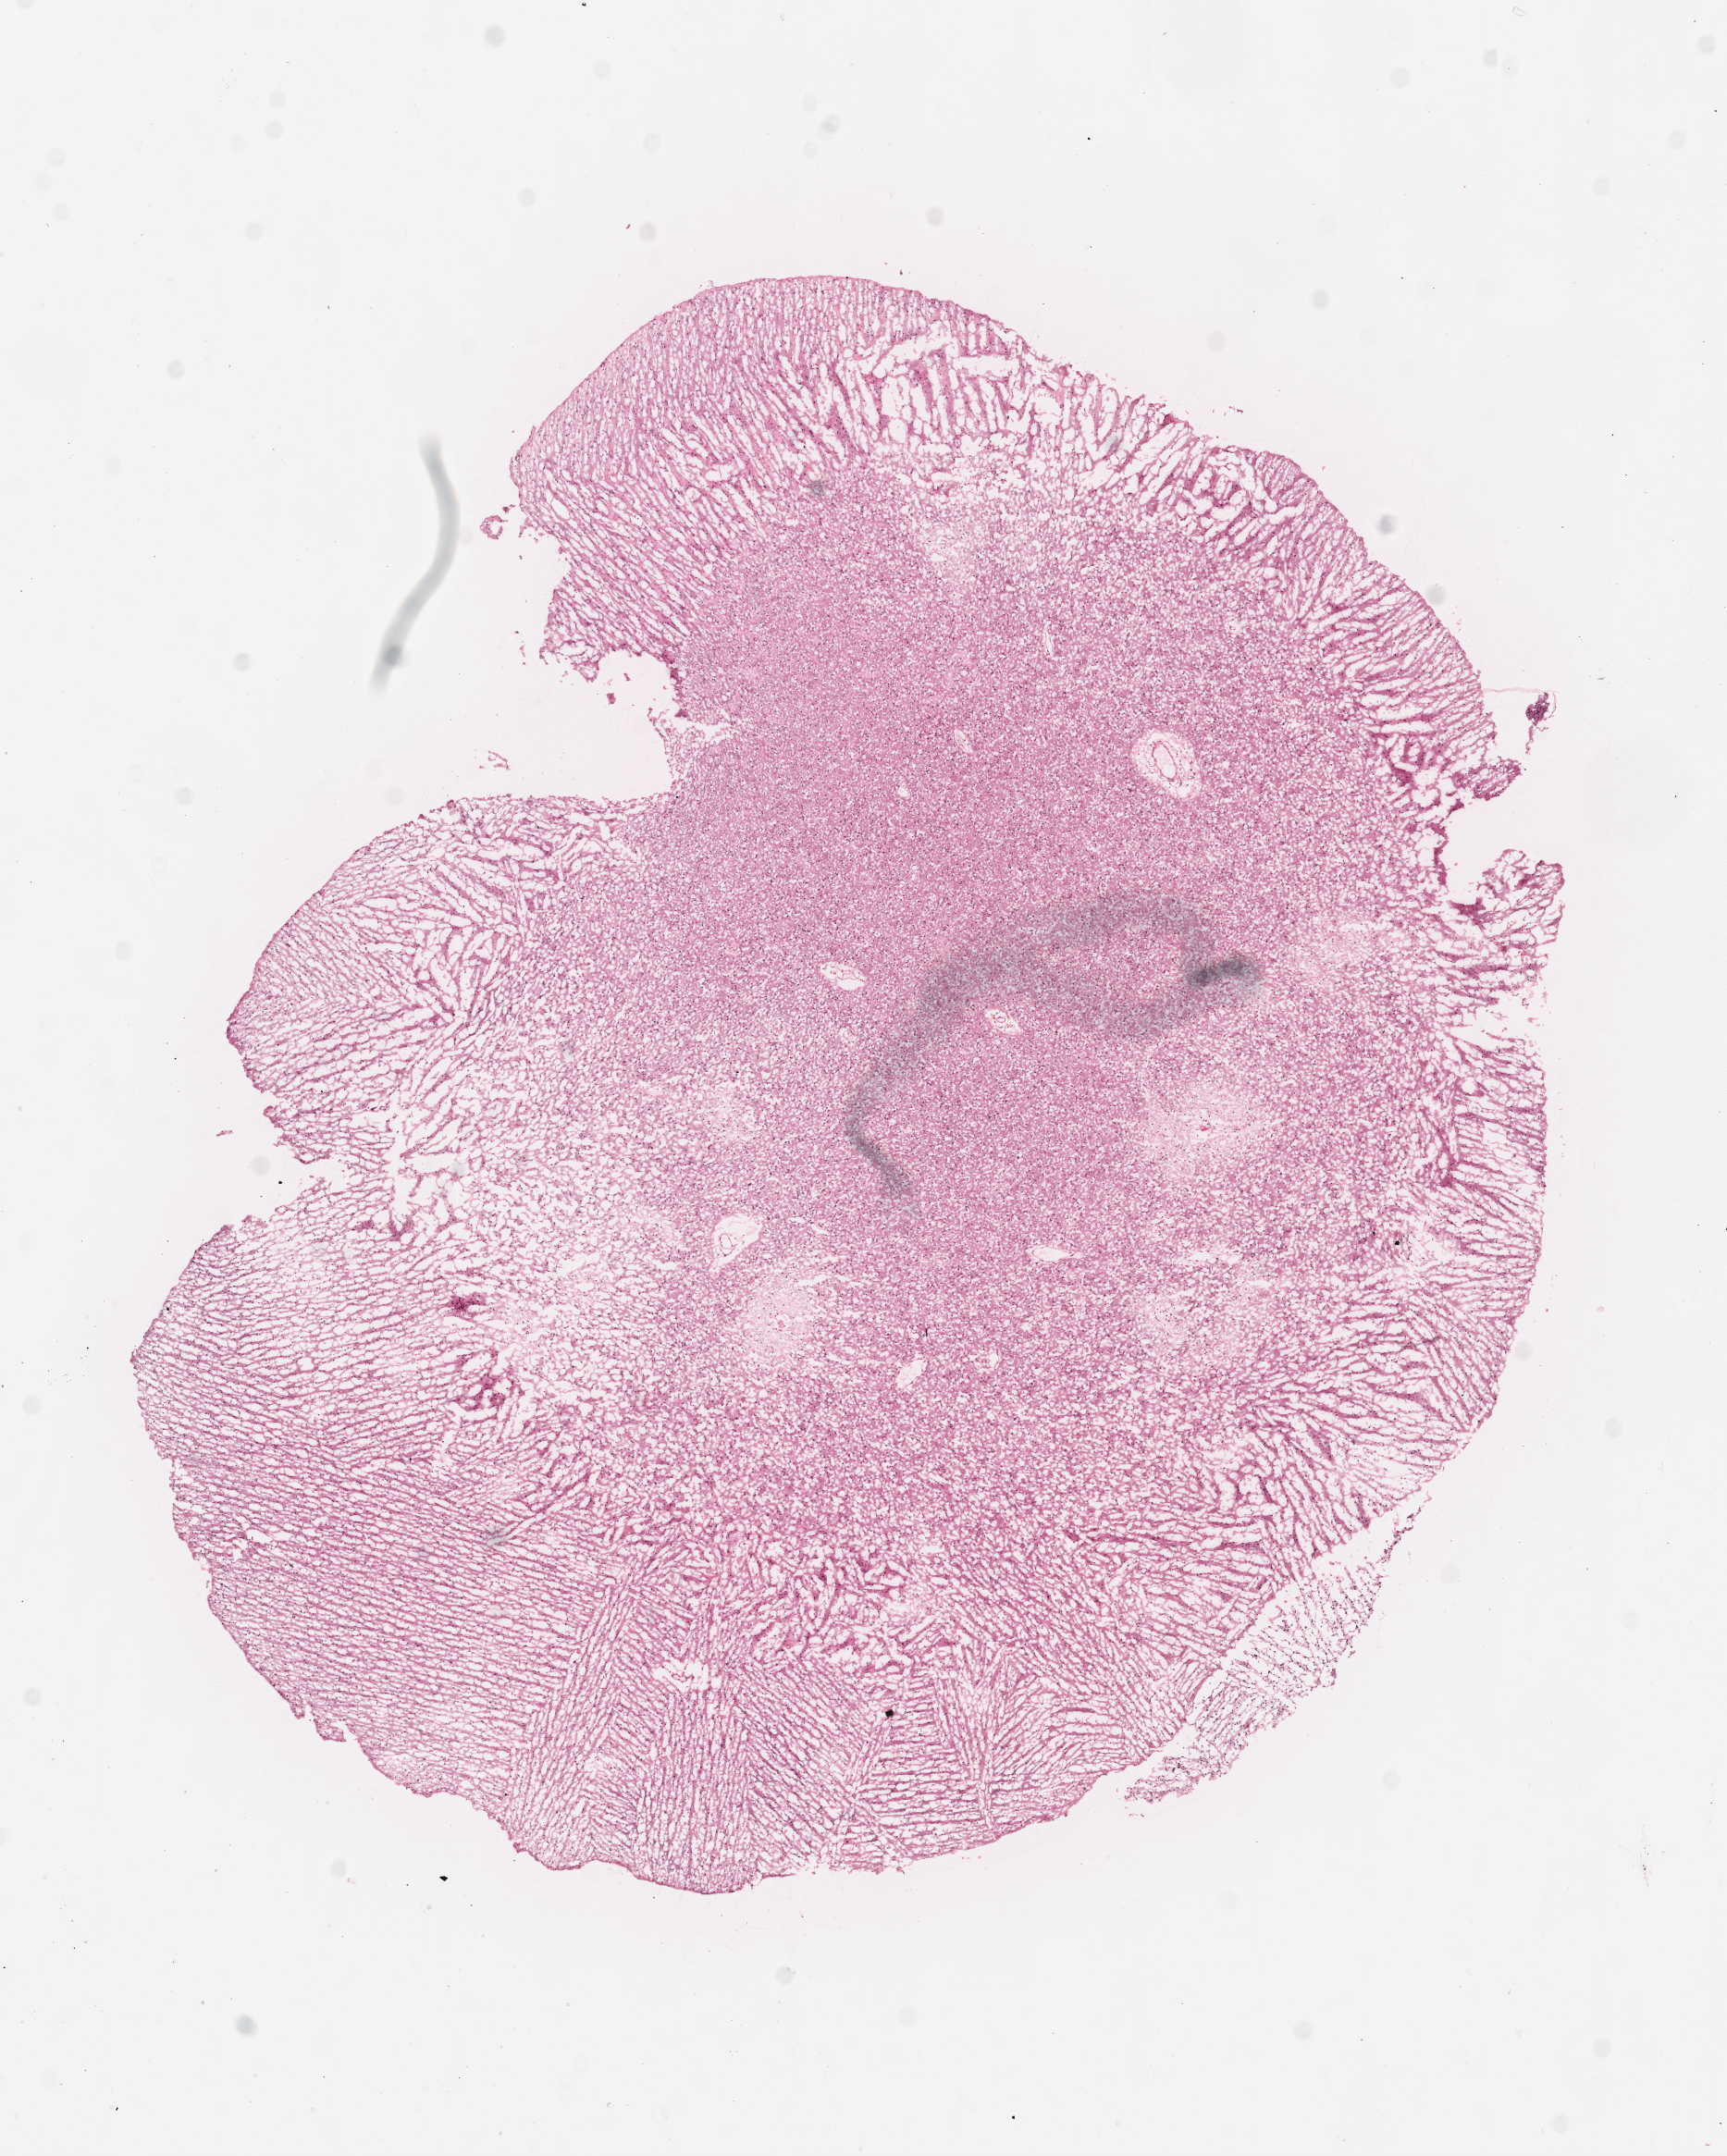
Digitized Hematoxylin and eosin (H&E) stained tissue section (whole slide), whole scanned area (about 7.3 x 9.2 mm, acquisition: 40x scan) shown as a low-resolution overview, frozen section from the top of the tissue portion, brain, primary tumour sample. Male, age 28 years at initial diagnosis.
Diagnosis: Oligodendroglioma, NOS (cerebrum).